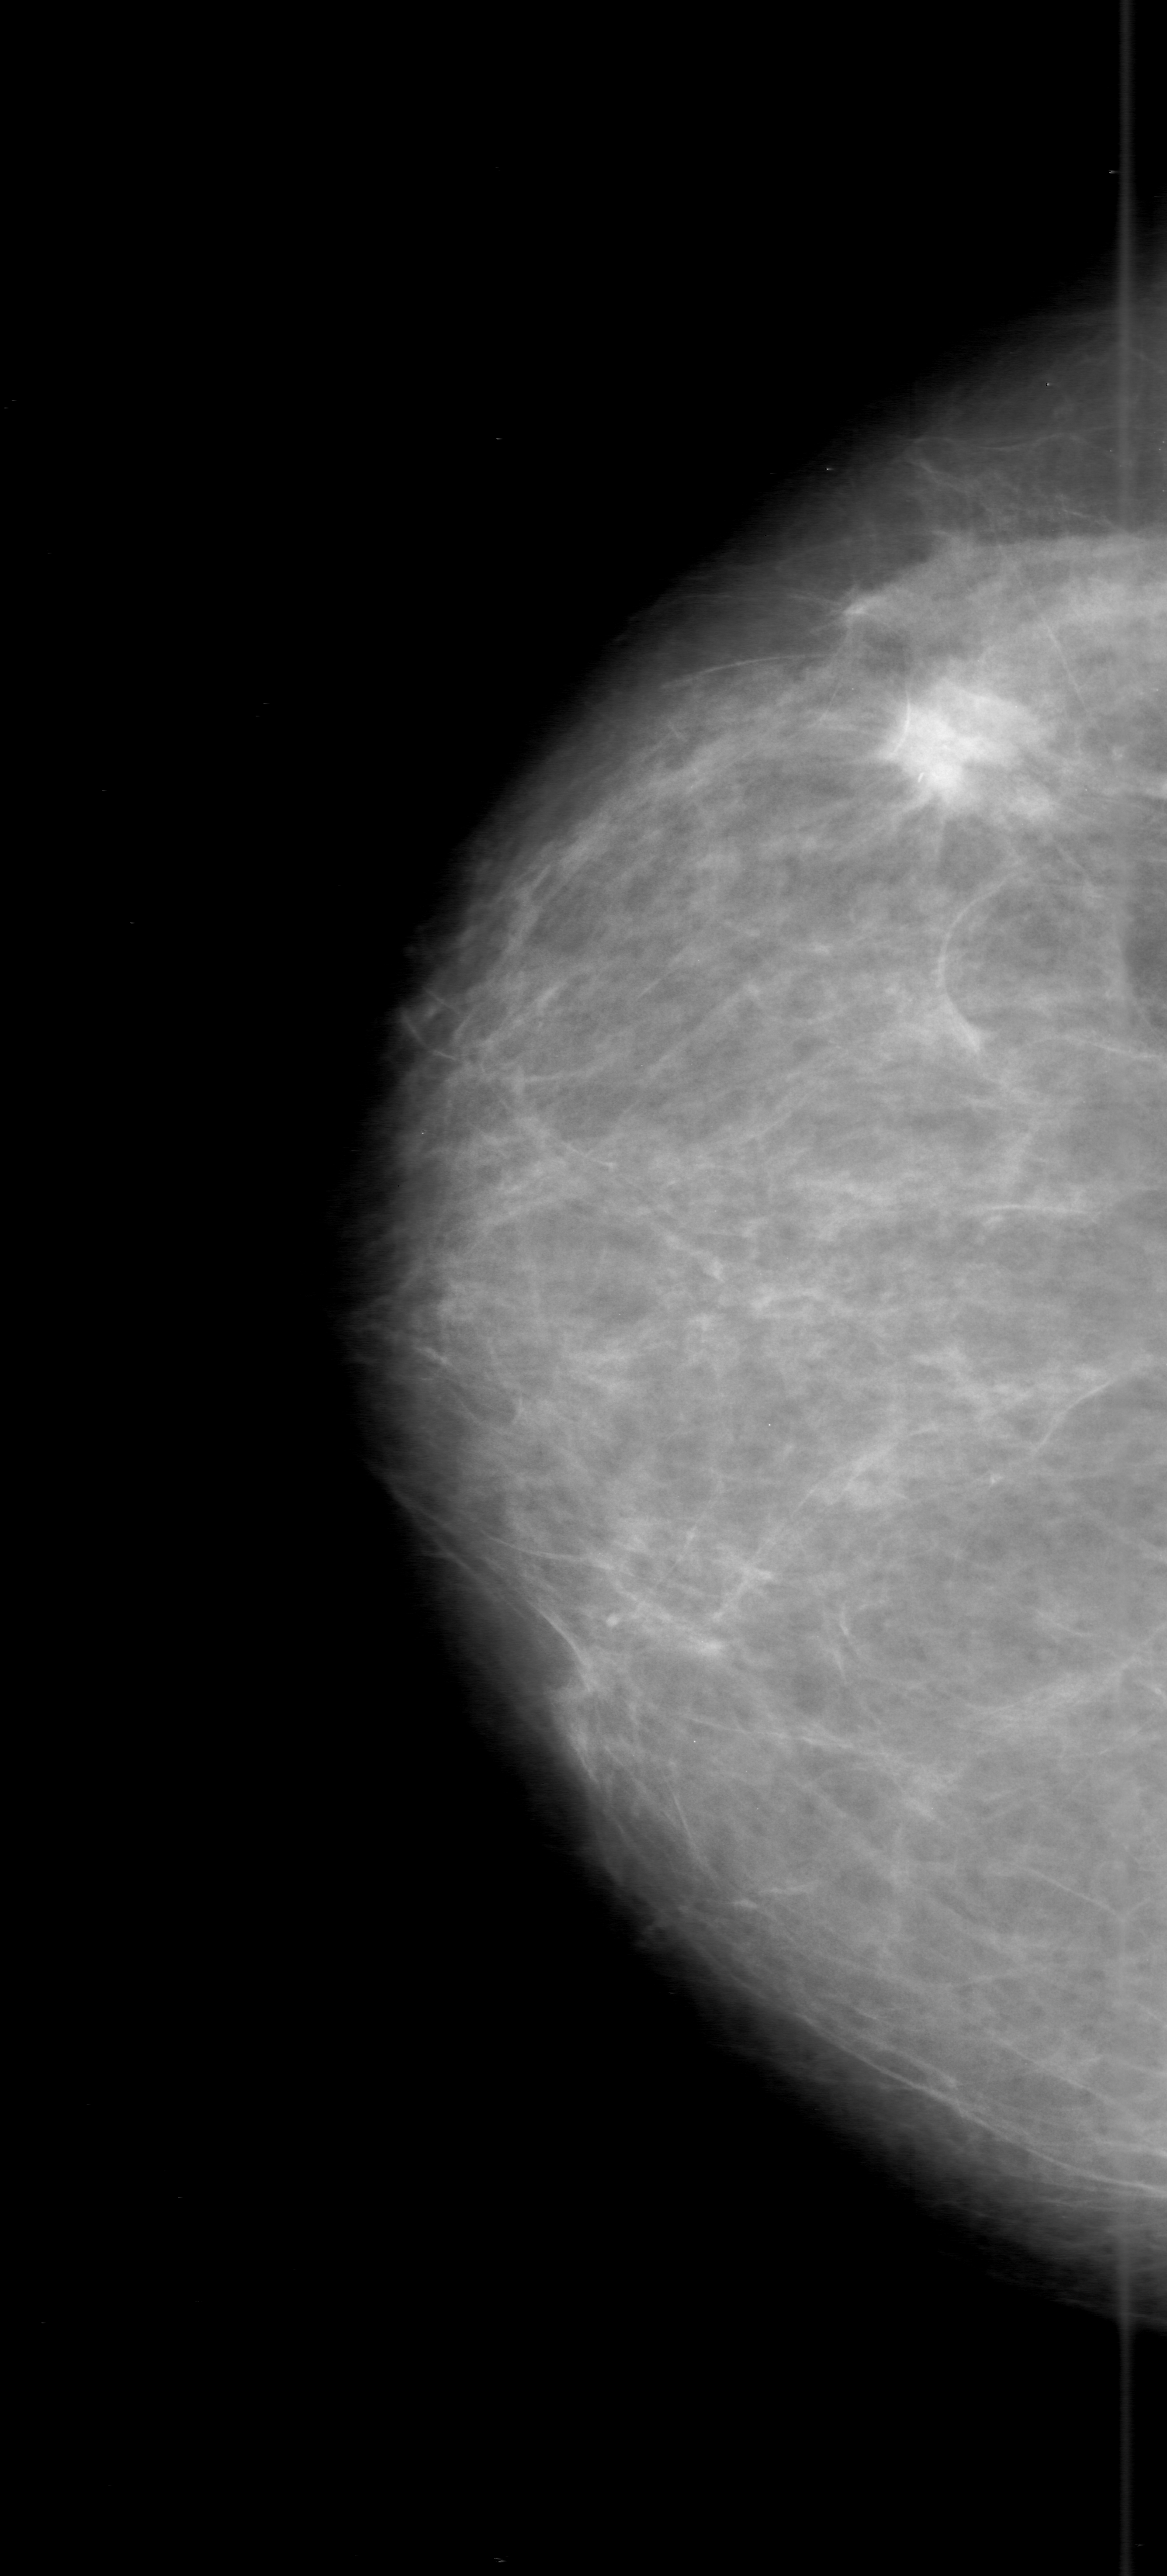
Mammogram (digitized film). Right breast. Craniocaudal (CC) view. Breast composition: scattered fibroglandular densities (BI-RADS density category 2 of 4). 1167 × 2576 image matrix.
Expert-marked regions of interest on this image (one box per marked abnormality):
- mass, shape irregular, margins obscured; BI-RADS assessment category 3; pathology (as recorded): malignant: bounding box (x1, y1, x2, y2) in pixels: (866, 646, 1060, 827)